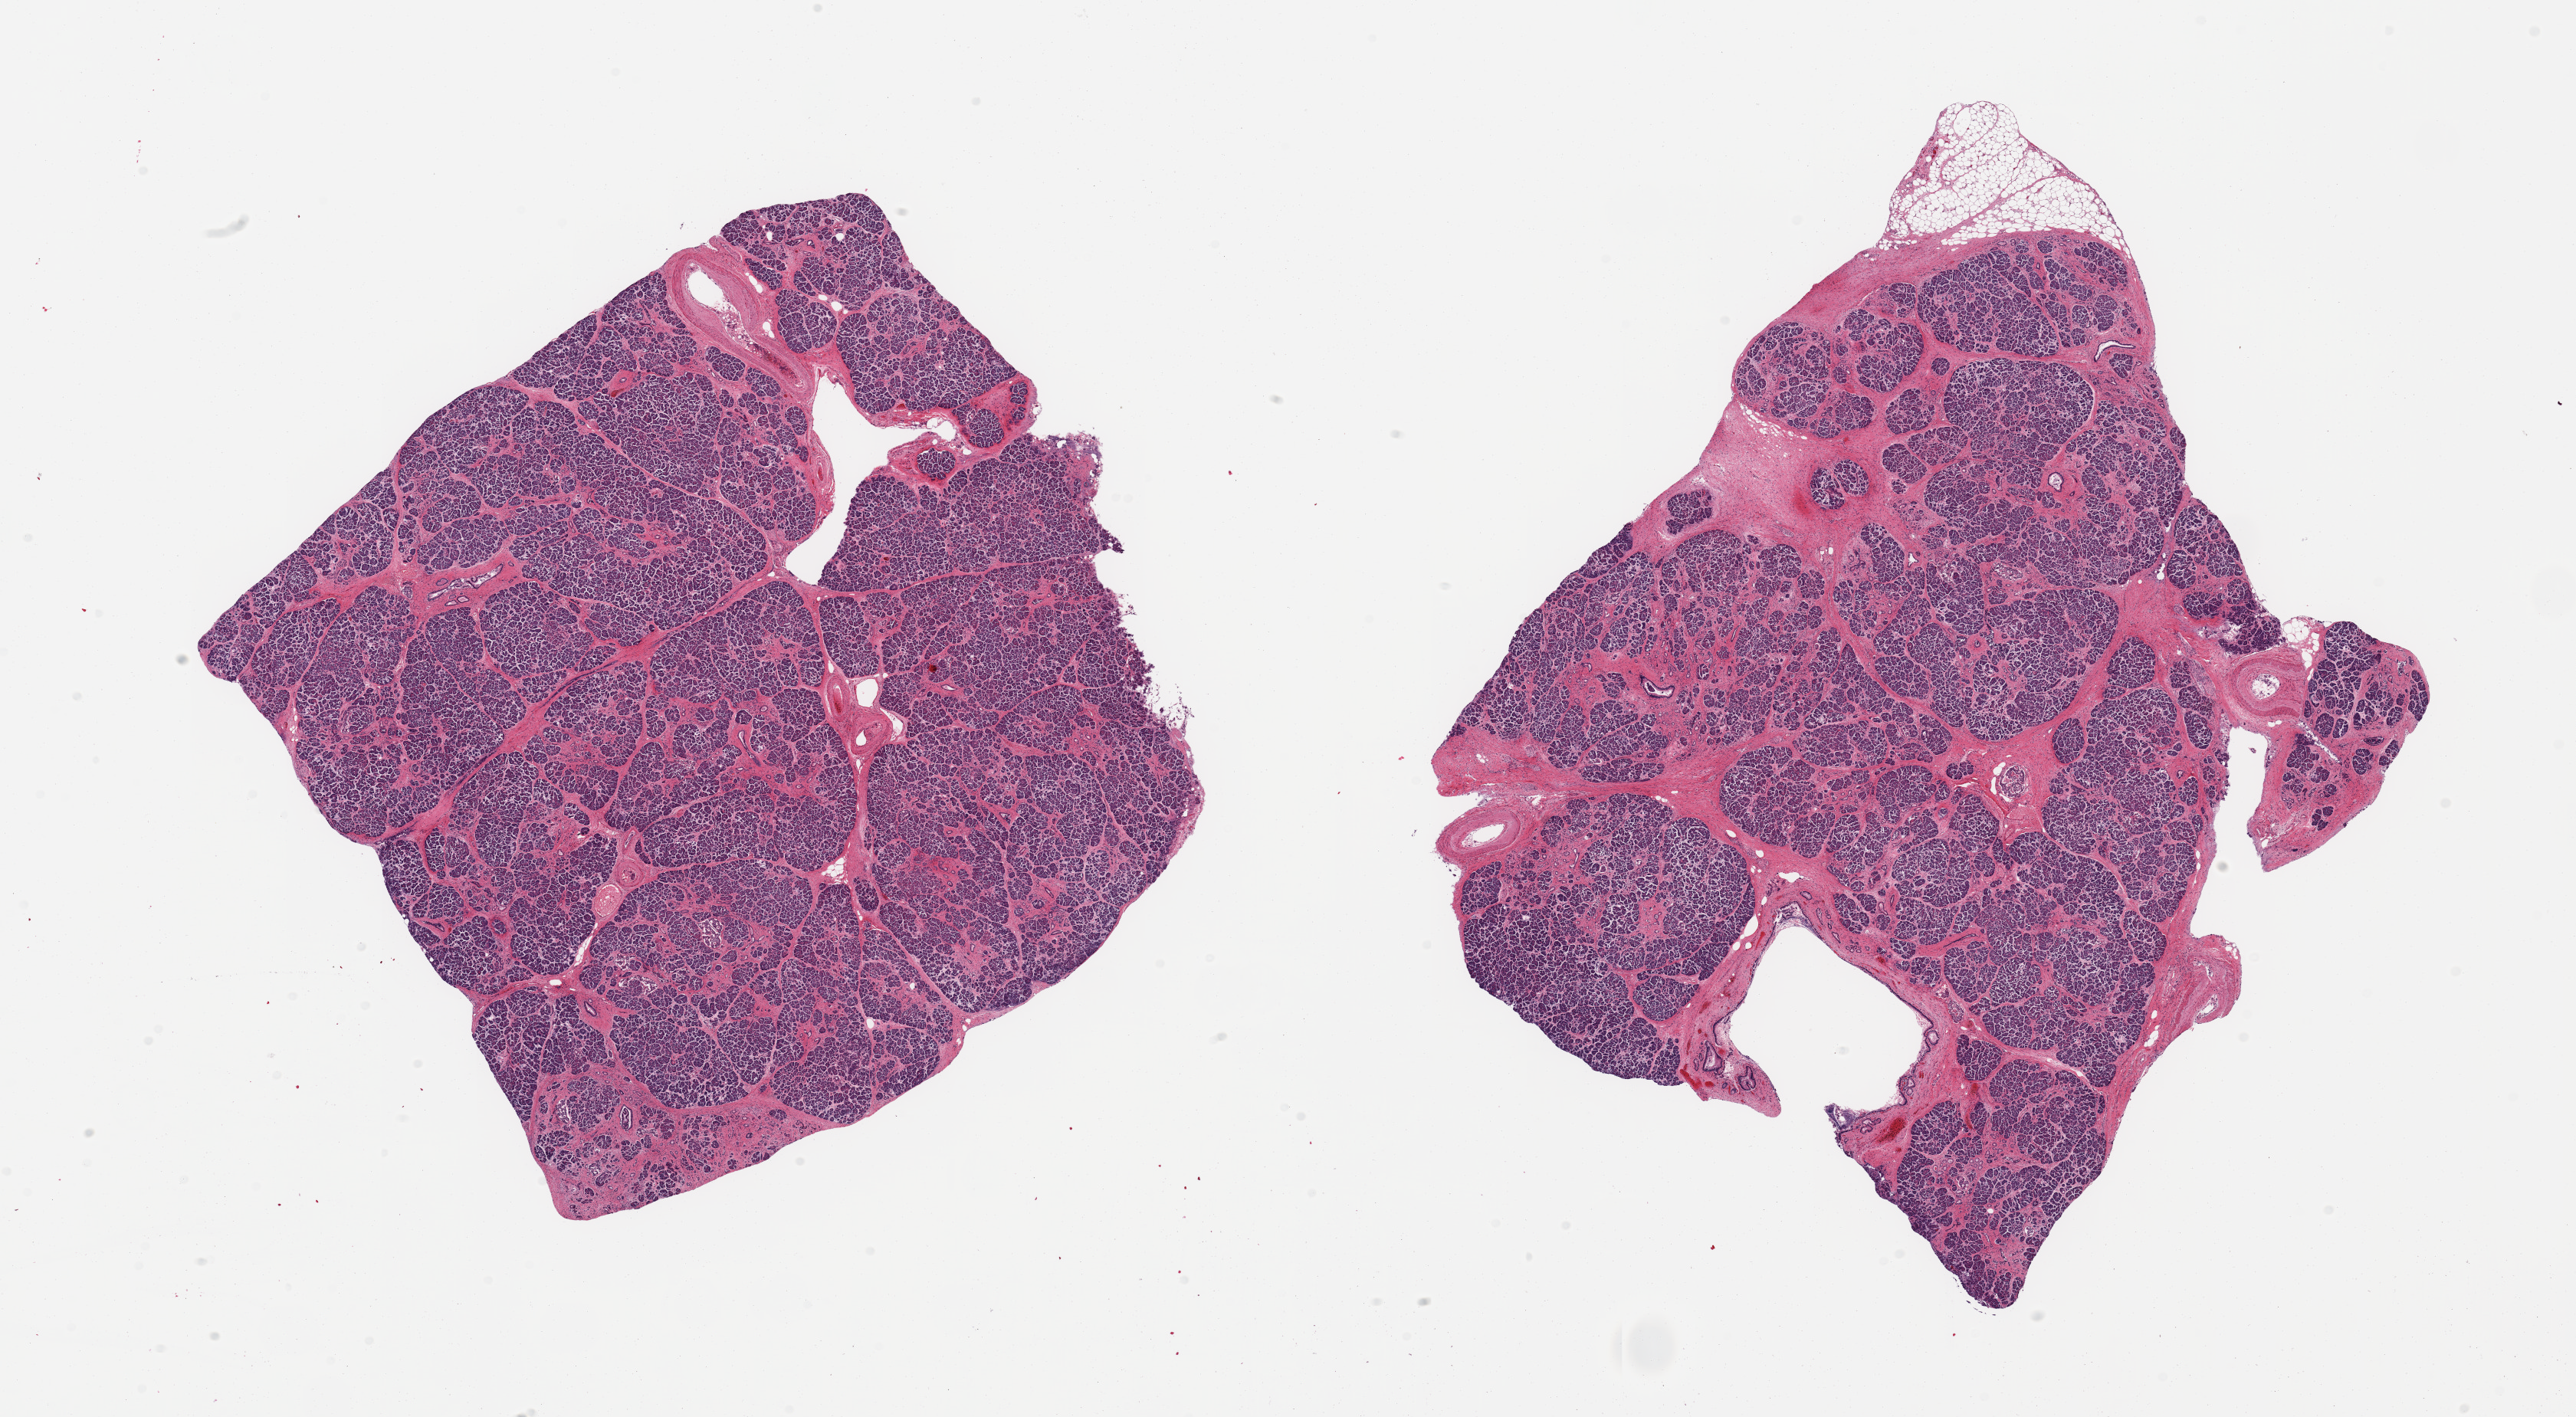
Hematoxylin and eosin (H&E) whole-slide image, brightfield — whole scanned area (about 26.6 x 14.6 mm) shown as a low-resolution overview. PAXgene-fixed paraffin-embedded (PFPE) section. Section of pancreas (target tissue). Tissue donor sample. Donor sex: male.
Review note (as recorded): 2 pieces; interstitial fibrosis with microlobulation; rare Langerhans islets; thick walled vessels.